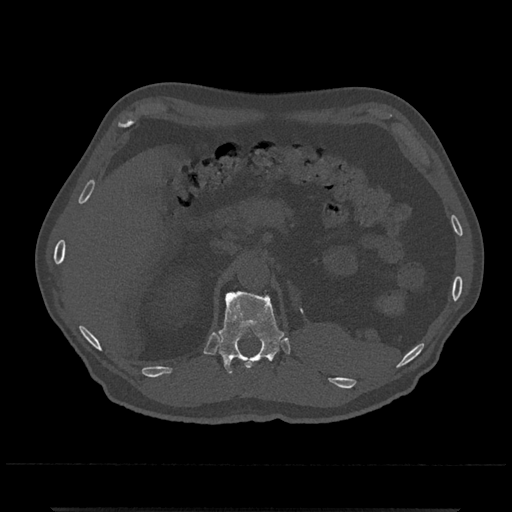
CT including the spine, one axial slice. Slice 439 of 797 in the series (ordered by position). Reconstruction kernel Br40s/3. 120 kVp. Bone window (W 1800 / L 400 HU). 0.5 mm slice thickness. 512 × 512 image matrix. Male patient, age 67 years. Case-level facts recorded for this patient, not image findings: primary cancer: prostate.
Outlined on this slice (semi-automatic segmentation, software-assisted and operator-edited):
- T11 vertebra: bounding box <252,361,255,365> (left, top, right, bottom; pixels)
- T12 vertebra: <218,290,284,373>